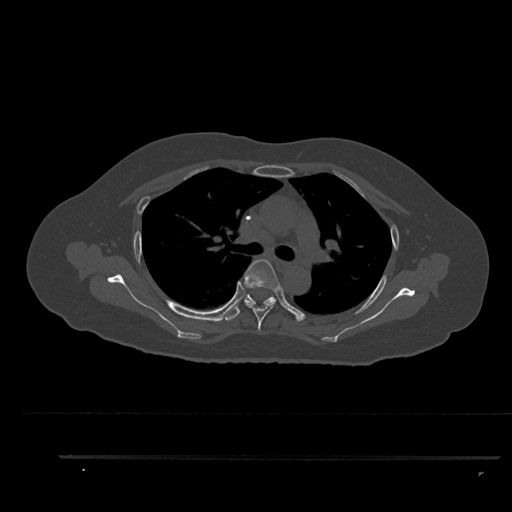
CT including the spine, one axial slice. Slice 625 of 797 in the series (ordered by position). 120 kVp. Bone window (W 1800 / L 400 HU). 512 × 512 image matrix. Patient: female, 44 years. Case-level facts recorded for this patient, not image findings: primary cancer: renal; vertebrae with lytic lesions (as recorded): L1.
Outlined on this slice (semi-automatic segmentation, software-assisted and operator-edited):
- T4 vertebra: bounding box <244,259,280,330> (left, top, right, bottom; pixels)
- T5 vertebra: <225,294,276,321>